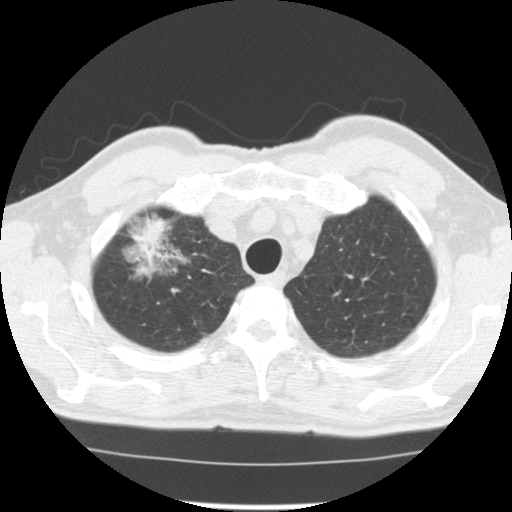
Axial slice from a low-dose chest CT screening exam; third screening round (two years after baseline); lung window (W 1500 / L -600 HU); 2.5 mm slice thickness; standard (soft-tissue) reconstruction kernel (STANDARD); slice 23 of 128 in the series; 512 × 512 image matrix, field of view 340 × 340 mm. Male participant, aged 64 years at enrolment.
Expert-annotated lung lesion, bounding box [x1, y1, x2, y2] px = [123, 228, 196, 289]. The screening reader recorded 3 non-calcified nodules or masses ≥4 mm on this exam; which of them this box marks is not recorded. Official screen result: positive, other. Later outcome: lung cancer diagnosed 30 days after this screen — adenocarcinoma, NOS, right upper lobe, well differentiated (G1), stage IB (AJCC 6th edition), 45 mm at pathology.